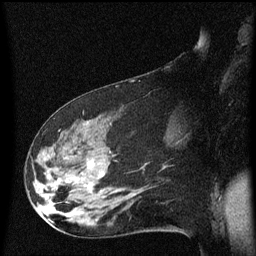
Breast MRI (dynamic contrast-enhanced), one sagittal slice. Slice 31 of 60 in the series (ordered by position). Dynamic contrast-enhanced series, image 2 of 3 at this slice position (ordered by acquisition). 1.5 T. TE 4.2 ms, TR 8.4 ms. 256 × 256 image matrix, field of view 200 × 200 mm. Patient: female, 48 years.
Outlined on this slice (semi-automatically segmented with operator editing):
- analysis volume of interest (the breast-tissue region the enhancement analysis was run in; not a lesion): bounding box (x1, y1, x2, y2) in pixels: (31, 116, 134, 225)
- tumour enhancement mask (voxels above the 70 % enhancement threshold inside the analysis volume of interest): (87, 162, 104, 175)